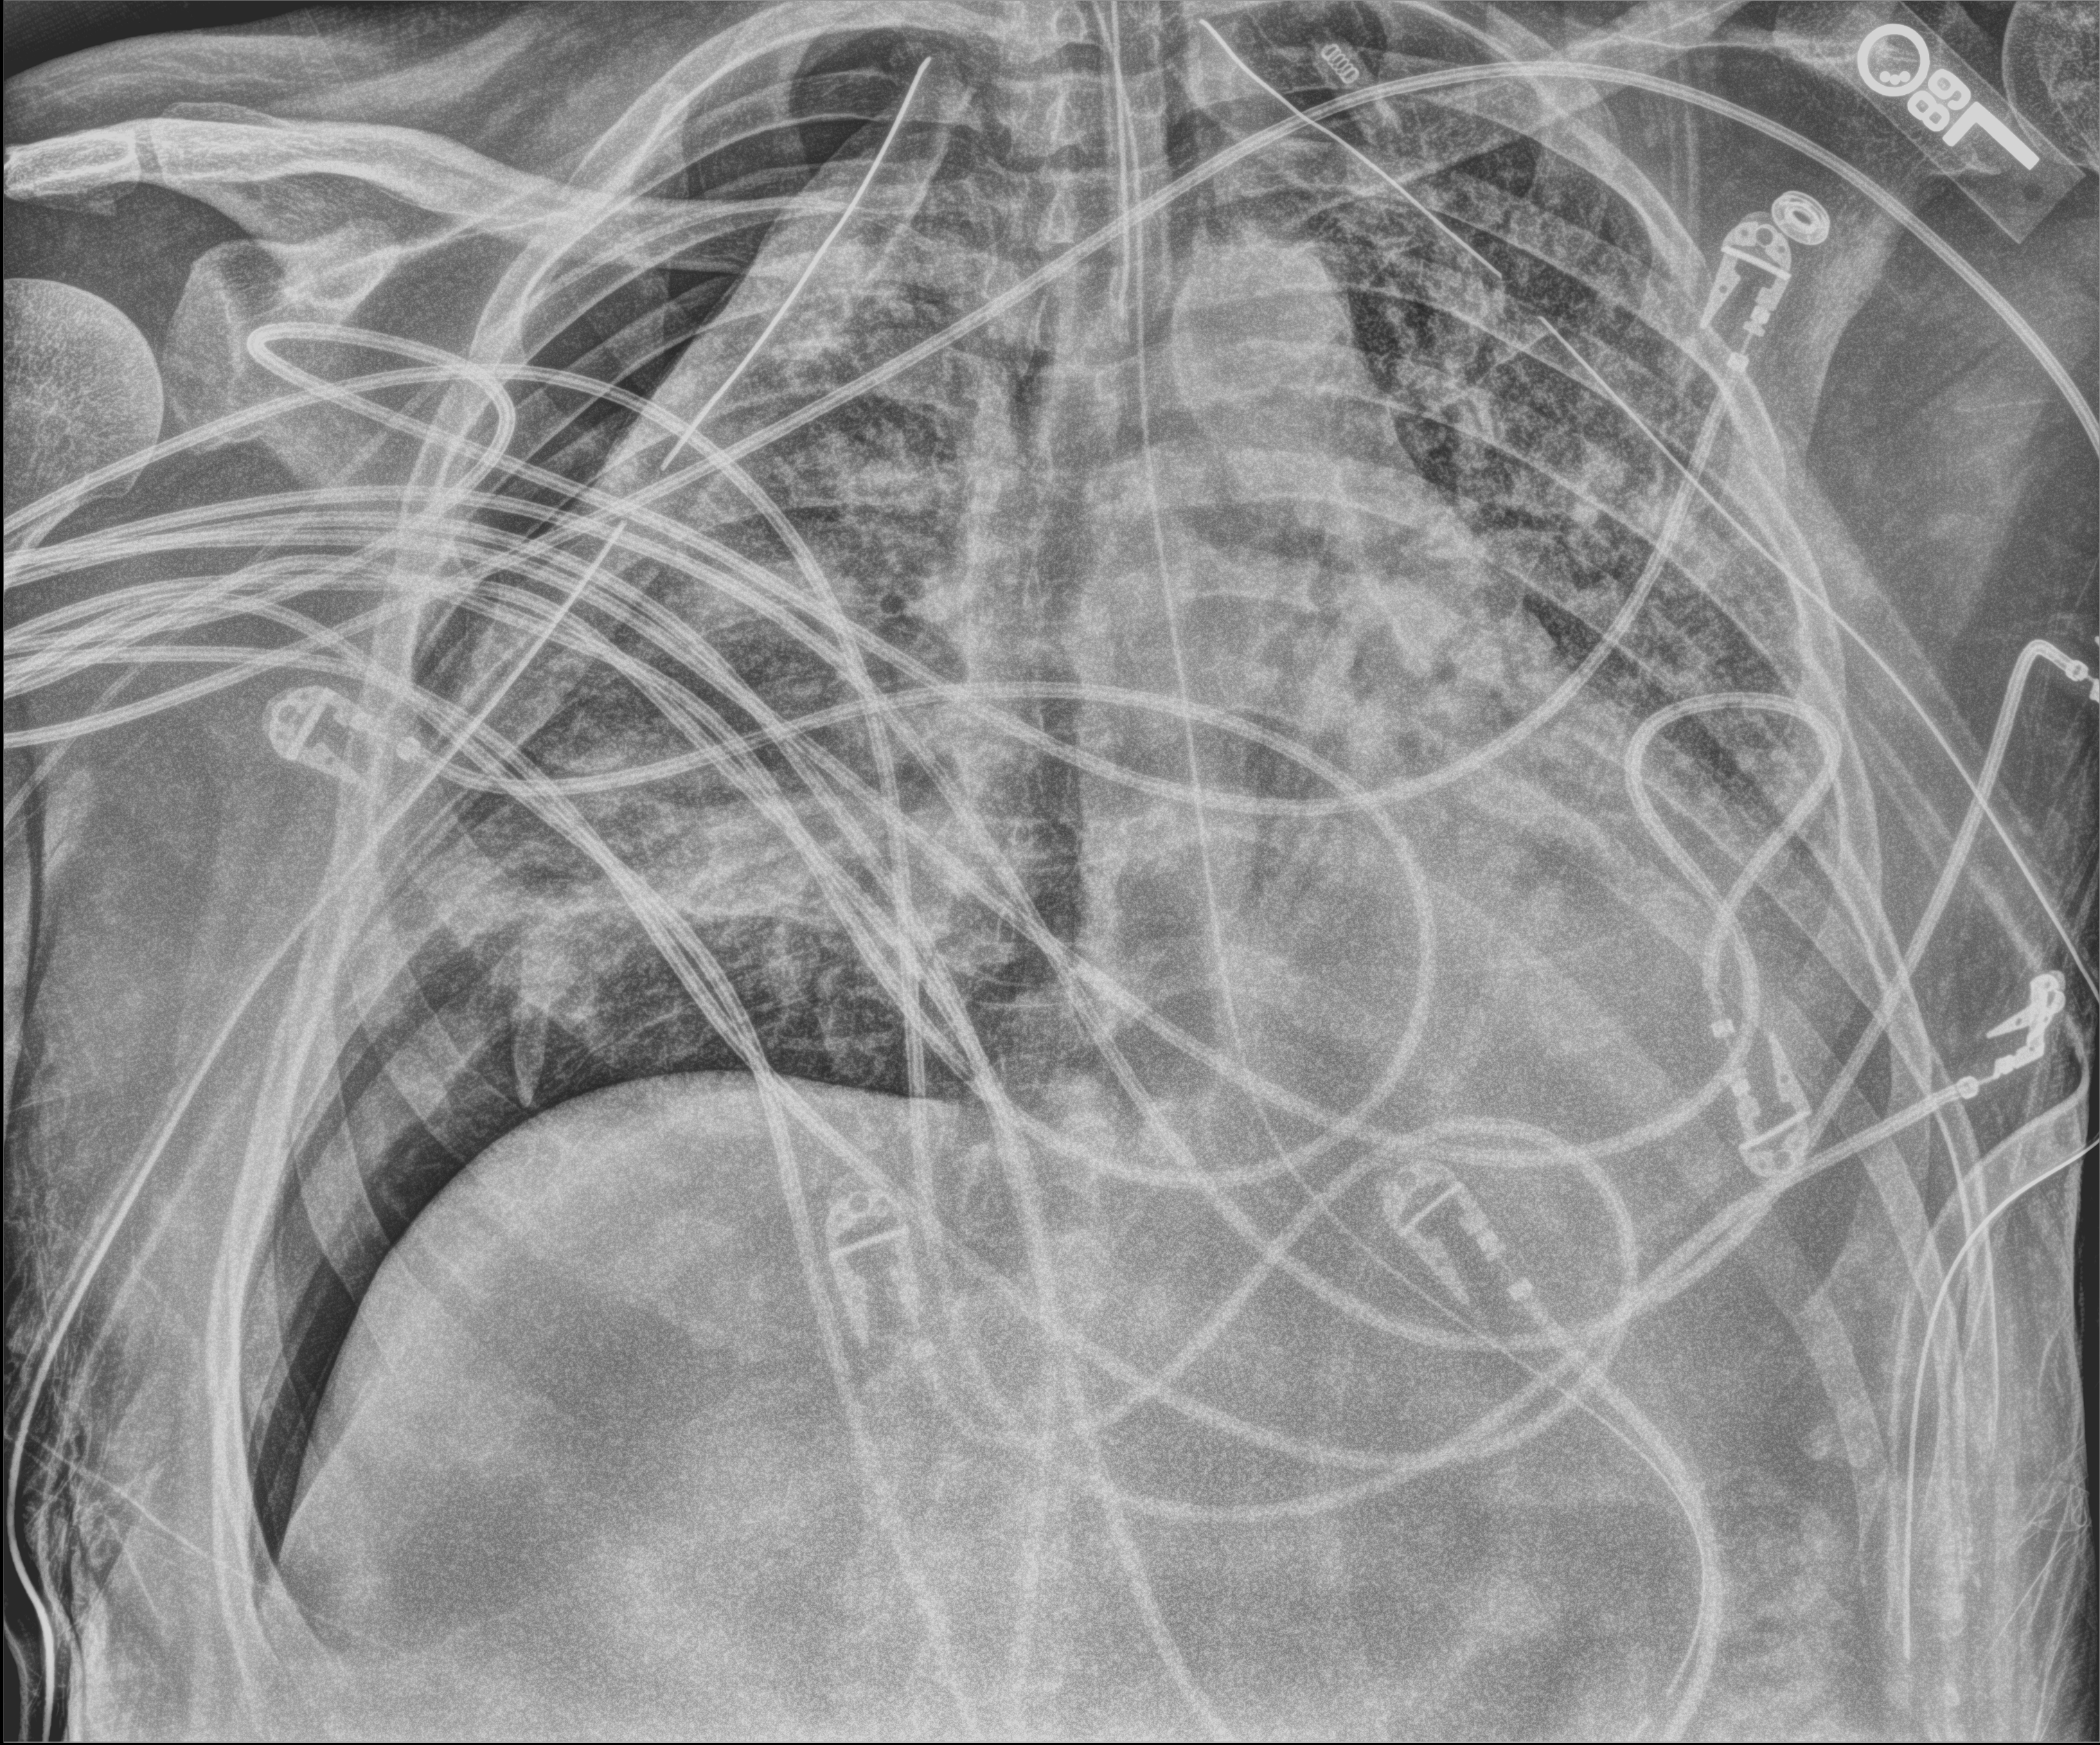
Bedside chest radiograph (digital radiography). Male patient hospitalised with COVID-19, age 18–59 years.
Admission-level facts for this patient (not findings on this image; timing relative to this image not recorded):
- COPD (admission record): no
- mechanically ventilated during this hospital stay: yes
- admitted to intensive care during this hospital stay: yes